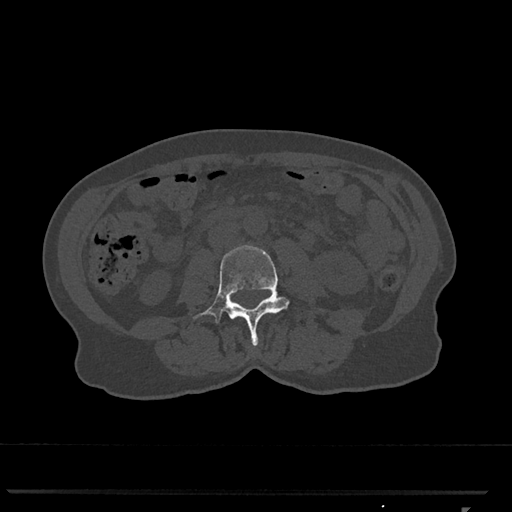
CT including the spine, one axial slice; slice 272 of 793 in the series (ordered by position); reconstruction kernel Br40s/3; 120 kVp; bone window (W 1800 / L 400 HU); 0.5 mm slice thickness; 512 × 512 image matrix, field of view 380 × 380 mm. Female patient, age 62 years. Case-level facts recorded for this patient, not image findings: primary cancer: renal.
Structures marked on this image (semi-automatically segmented with operator editing):
- L3 vertebra: box from (x=193, y=245) to (x=290, y=346) px